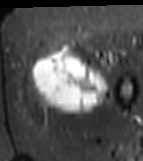
MRI of an extremity soft-tissue mass, one axial slice; slice 21 of 81 in the series (ordered by position); STIR; MR volume resampled by the dataset authors to the PET/CT grid (not the native acquisition matrix); 143 × 161 image matrix, field of view 140 × 157 mm. Female patient. From the clinical record (not read from this slice): histological type: myxofibrosarcoma; grade: intermediate; site of the primary tumour: left thigh.
Annotated regions visible in this slice (expert contour drawn on MRI and transferred to this co-registered scan by the dataset authors):
- gross tumour volume including surrounding oedema: bounding box [x1, y1, x2, y2] px = [28, 44, 112, 114]
- gross tumour volume (mass): [31, 47, 111, 114]